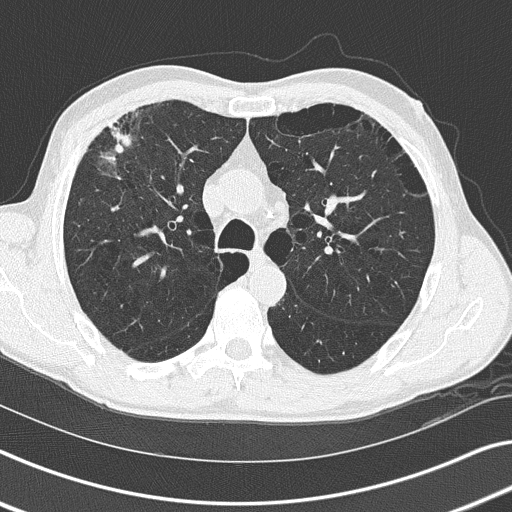
Low-dose screening chest CT, axial slice; third annual screen; lung window (W 1500 / L -600 HU); slice 62 of 170 in the series. Male, age 66 years at enrolment. Current smoker at enrolment.
- Lesion marked by an expert reader, box from (x=79, y=104) to (x=154, y=188) px.
- The exam's reader record, not a measurement of the box and not confirmed to be the same lesion: non-calcified nodule or mass ≥4 mm, left lower lobe, 9 × 8 mm, smooth margins, soft tissue attenuation, pre-existing on the prior screen: yes; interval growth: no.
- Note: the box lies in the patient's right hemithorax on this image, whereas the reader's record names the left lung; they may be different findings.